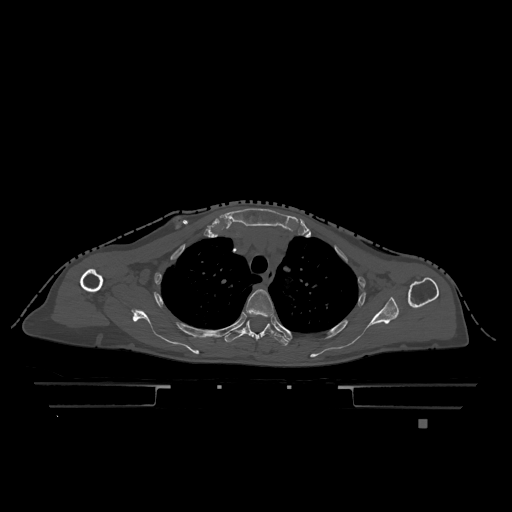
CT including the spine, one axial slice. Bone window (W 1800 / L 400 HU). 512 × 512 image matrix, field of view 500 × 500 mm. Patient: female, 74 years. From the clinical record (not read from this slice): primary cancer: lung.
Outlined on this slice (semi-automatic segmentation, software-assisted and operator-edited):
- T3 vertebra: bounding box [x1, y1, x2, y2] px = [246, 289, 274, 317]
- T4 vertebra: [224, 316, 292, 346]